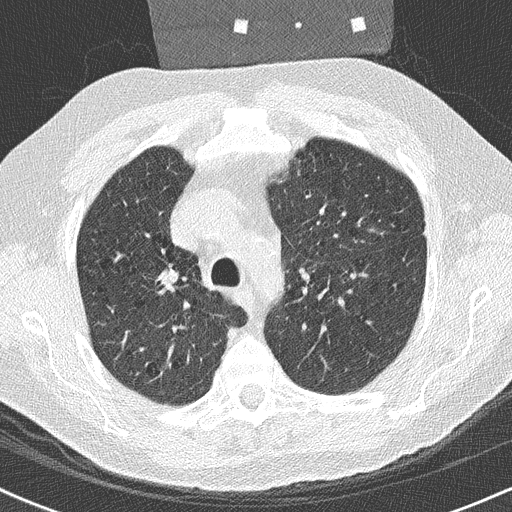
Chest CT (low-dose screening protocol), one axial image; baseline annual screen; lung window (W 1500 / L -600 HU); 2 mm slice thickness; 512 × 512 image matrix, field of view 314 × 314 mm. Male, age 59 years at enrolment.
Expert reader's lesion annotation, bounding box [x1, y1, x2, y2] px = [147, 259, 186, 297]. Screening reader's record for this exam: no non-calcified nodule ≥4 mm recorded. Official screen result: negative screen, minor abnormalities not suspicious for lung cancer.